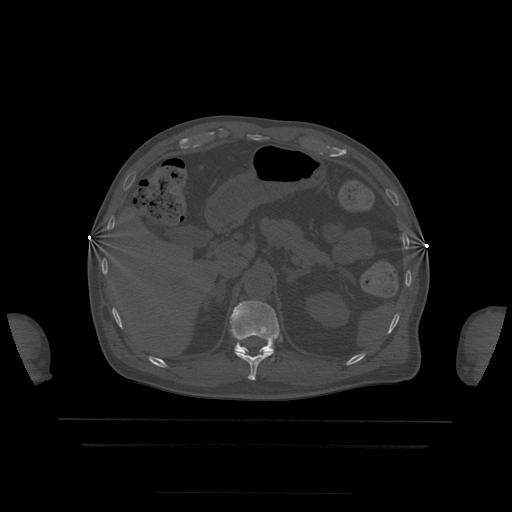
CT including the spine, one axial slice. Position 208 of 522 along the scan axis. Bone window (W 1800 / L 400 HU). 1.25 mm slice thickness. 512 × 512 image matrix, field of view 436 × 436 mm. Patient age 68 years. Case-level facts recorded for this patient, not image findings: primary cancer: urothelial.
Outlined on this slice (semi-automatic segmentation, software-assisted and operator-edited):
- T11 vertebra: bounding box (x1, y1, x2, y2) in pixels: (234, 351, 274, 381)
- T12 vertebra: (230, 300, 280, 354)